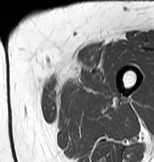
MRI of an extremity soft-tissue mass, one axial slice; slice 8 of 83 in the series (ordered by position); MR volume resampled by the dataset authors to the PET/CT grid (not the native acquisition matrix); 3.27 mm slice thickness; 154 × 162 image matrix, field of view 150 × 158 mm. Female patient. From the clinical record (not read from this slice): histological type: myxofibrosarcoma; grade: intermediate; site of the primary tumour: left thigh.
Outlined on this slice (expert contour drawn on MRI and transferred to this co-registered scan by the dataset authors):
- gross tumour volume including surrounding oedema: box from (x=44, y=61) to (x=111, y=101) px